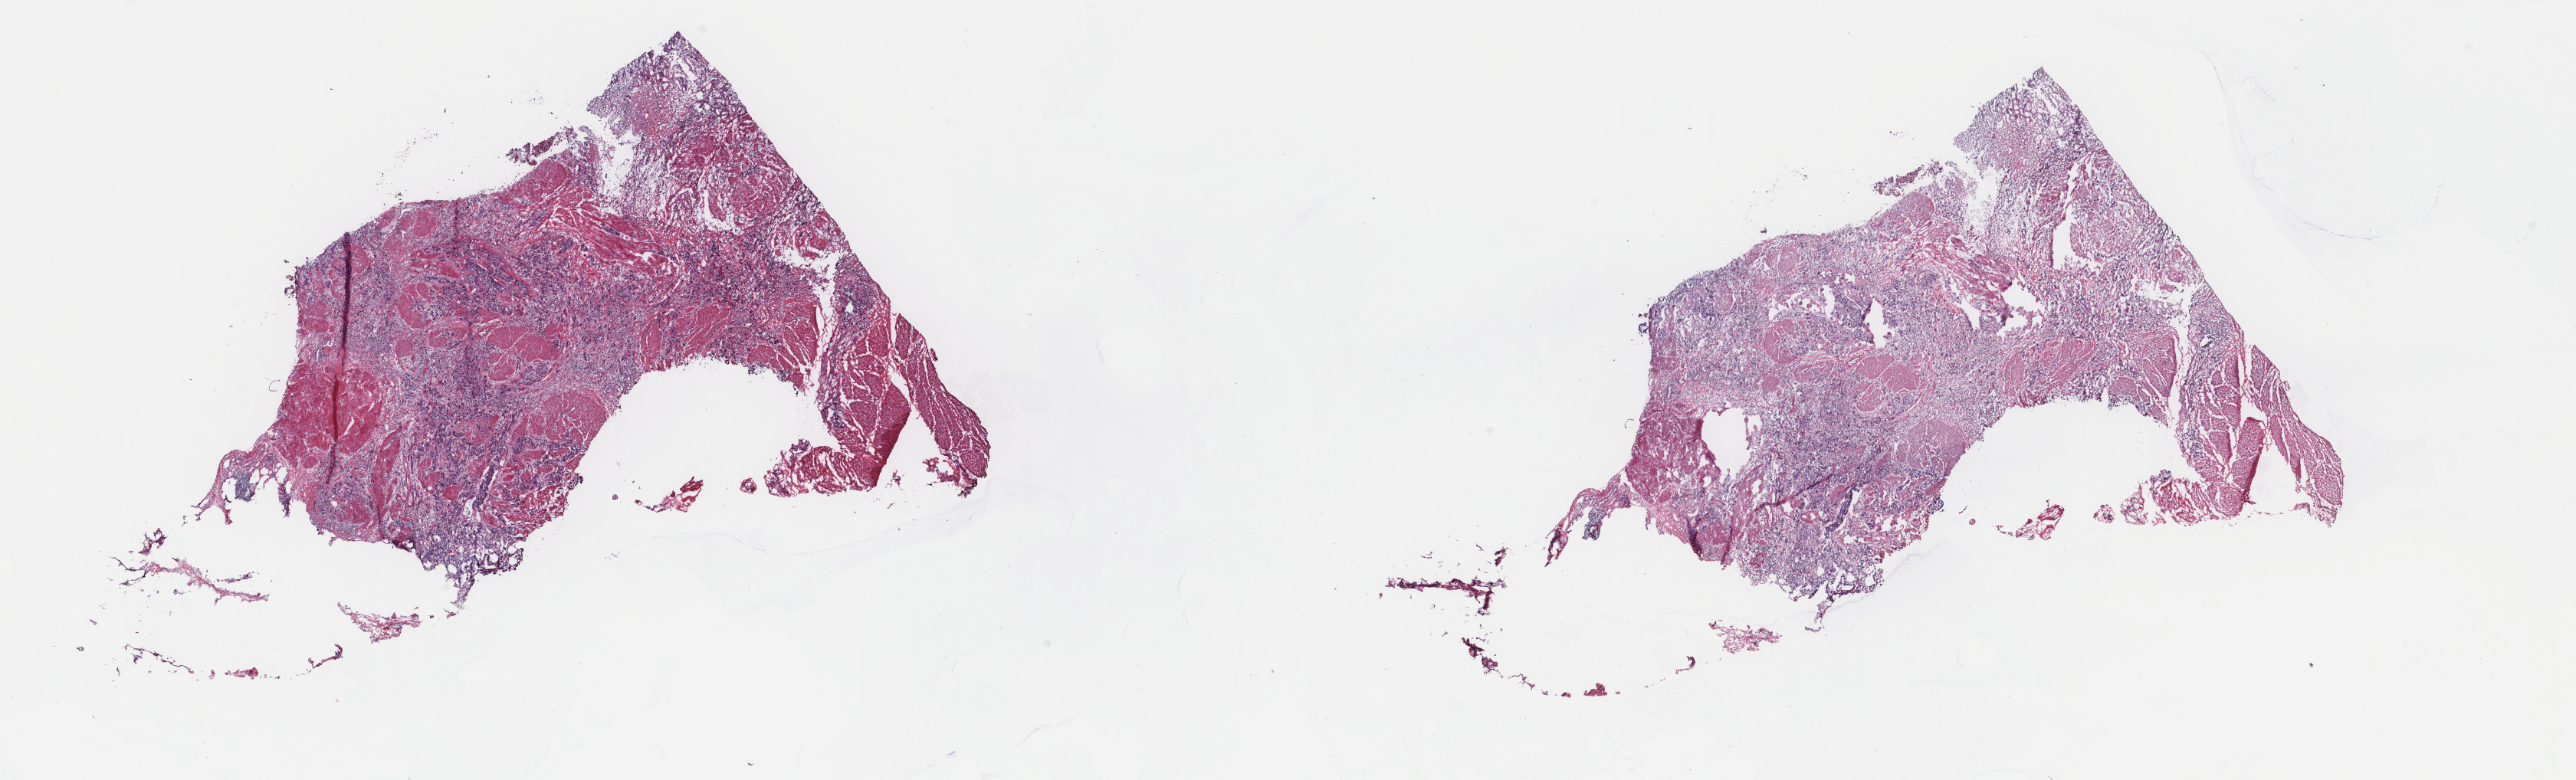
Digitized H&E-stained tissue section (whole slide) — a low-resolution overview of the entire scanned area, about 26.7 x 8.1 mm (acquisition: 40x scan); frozen section from the top of the tissue portion; bladder, primary tumour sample. Patient: male, age at initial diagnosis 62 years. Histologic grade: high grade. Slide review estimates, as recorded: tumour cells 60%, tumour nuclei 70%, normal cells 40%, stromal cells 0%, necrosis 0%. Inflammatory infiltration, as recorded: lymphocyte infiltration 2%, monocyte infiltration 0%, neutrophil infiltration 0%.
Pathologic diagnosis: Transitional cell carcinoma (lateral wall of bladder). Lymph nodes positive (case pathology): 0 of 7 examined. AJCC pathologic stage: III (6th edition). TNM: T3 N0 M0.